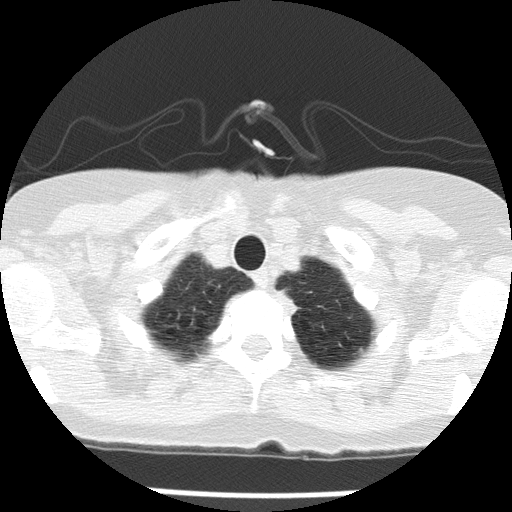
Axial slice from a low-dose chest CT screening exam; baseline screening round; lung window (W 1500 / L -600 HU); slice 13 of 143 in the series. Female participant, aged 74 years at enrolment. Former smoker at enrolment.
Expert-annotated lung lesion, bounding box <266,286,307,321> (left, top, right, bottom; pixels). The screening reader recorded 2 non-calcified nodules or masses ≥4 mm on this exam; which of them this box marks is not recorded. Official screen result: positive, change unspecified: nodule(s) >= 4 mm or enlarging nodule(s), mass(es), or other non-specific abnormalities suspicious for lung cancer. Participant outcome: lung cancer diagnosed 81 days after this screen — adenocarcinoma, NOS, left upper lobe, poorly differentiated (G3), stage IA (AJCC 6th edition), 24 mm at pathology.